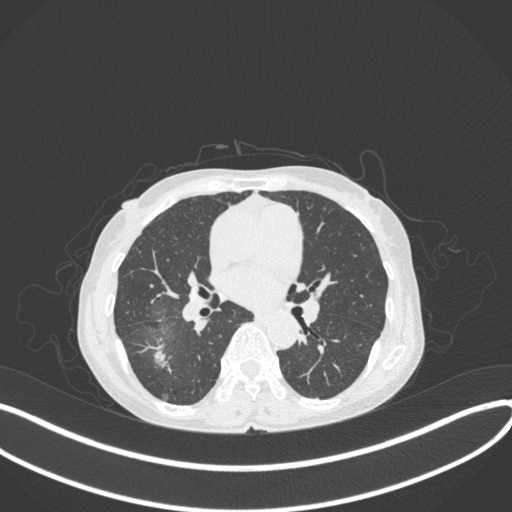
Chest CT, one axial slice. Slice 204 of 379 in the series (ordered by position). Reconstruction kernel B31f. 120 kVp. Lung window (W 1500 / L -600 HU). 512 × 512 image matrix, field of view 400 × 400 mm. Female patient, age 69 years. From the clinical record (not read from this slice): clinical TNM (as recorded): T1b N0 M0.
Outlined on this slice (bounding box drawn by a radiologist):
- lung tumour (recorded histology: adenocarcinoma): box from (x=150, y=339) to (x=175, y=371) px